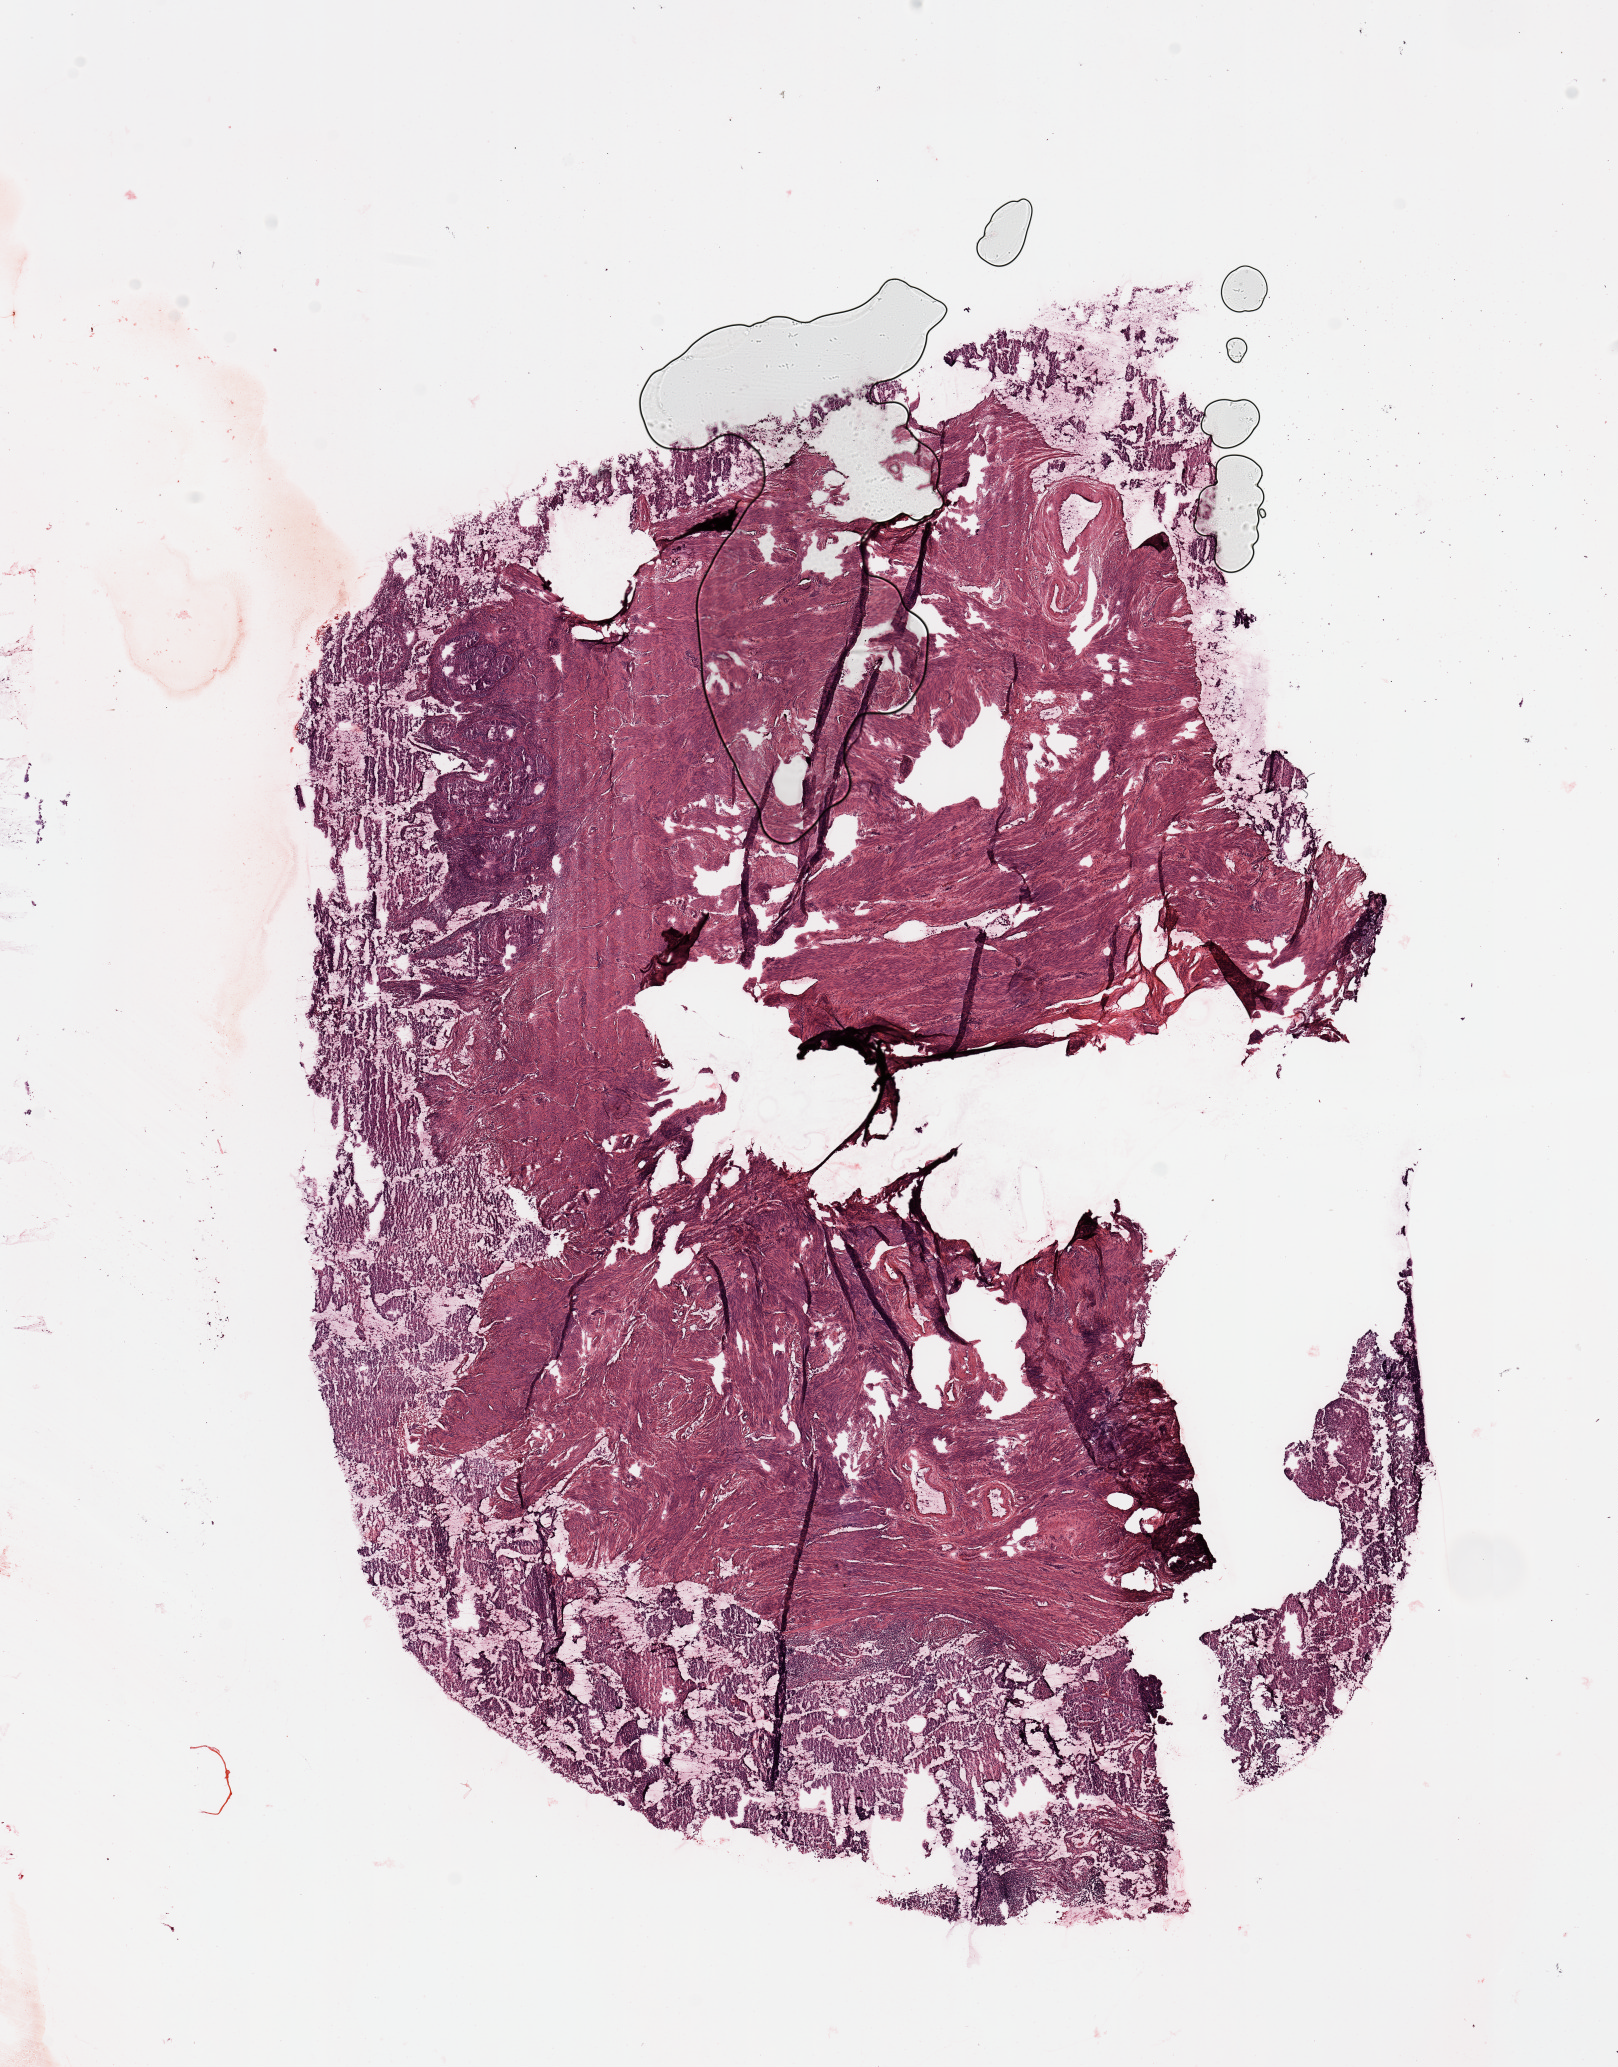
Whole-slide histology image, Hematoxylin and eosin (H&E) stained, shown as a low-resolution overview of the whole scanned area (about 12.8 x 16.3 mm, acquisition: 20x scan), tumour tissue sample, uterus. Patient: female, age 45 years. Histologic grade: G2 (moderately differentiated).
• AJCC pathologic stage: I
• histologic diagnosis: Endometrioid adenocarcinoma, NOS